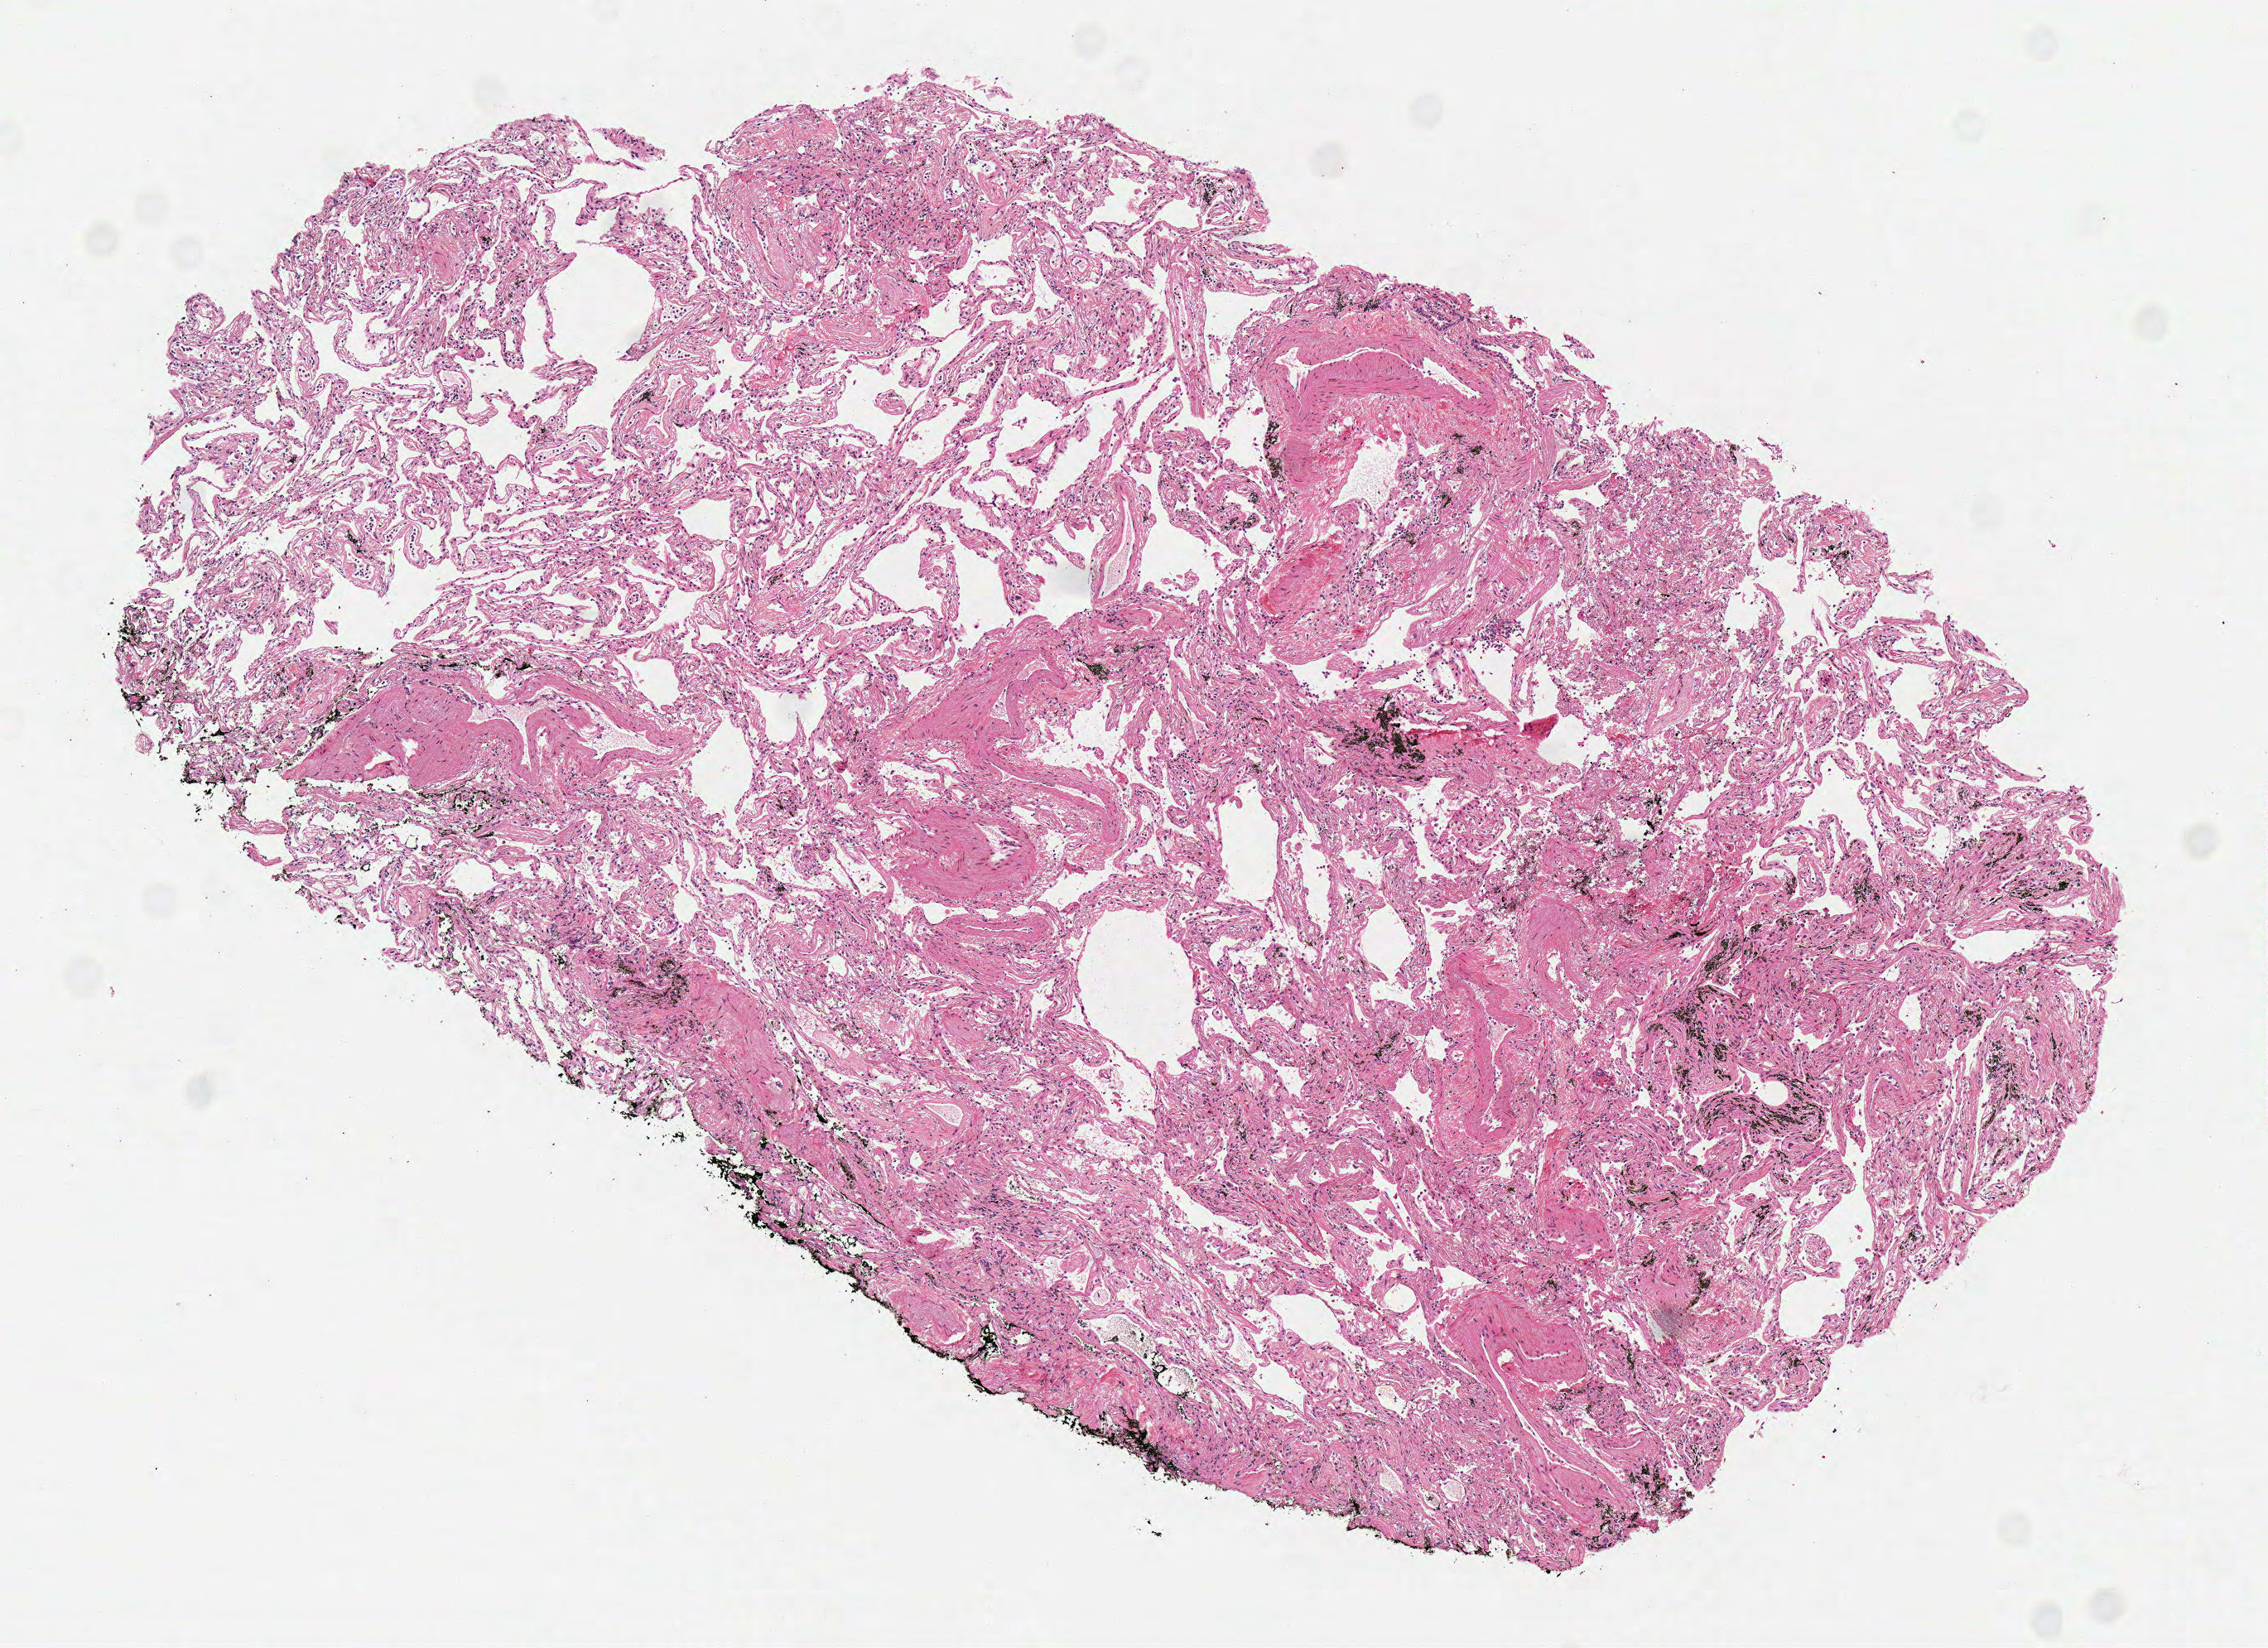
Digitized Hematoxylin and eosin (H&E) stained tissue section (whole slide) — shown as a low-resolution overview of the whole scanned area (about 5.4 x 3.9 mm, slide scanned at 40x); frozen section from the top of the tissue portion; sample: solid tissue normal (non-tumour tissue), lung. Male, age 84 years at initial diagnosis.
This section: solid tissue normal sample (biorepository sample class). Patient diagnosis: Adenocarcinoma, NOS.